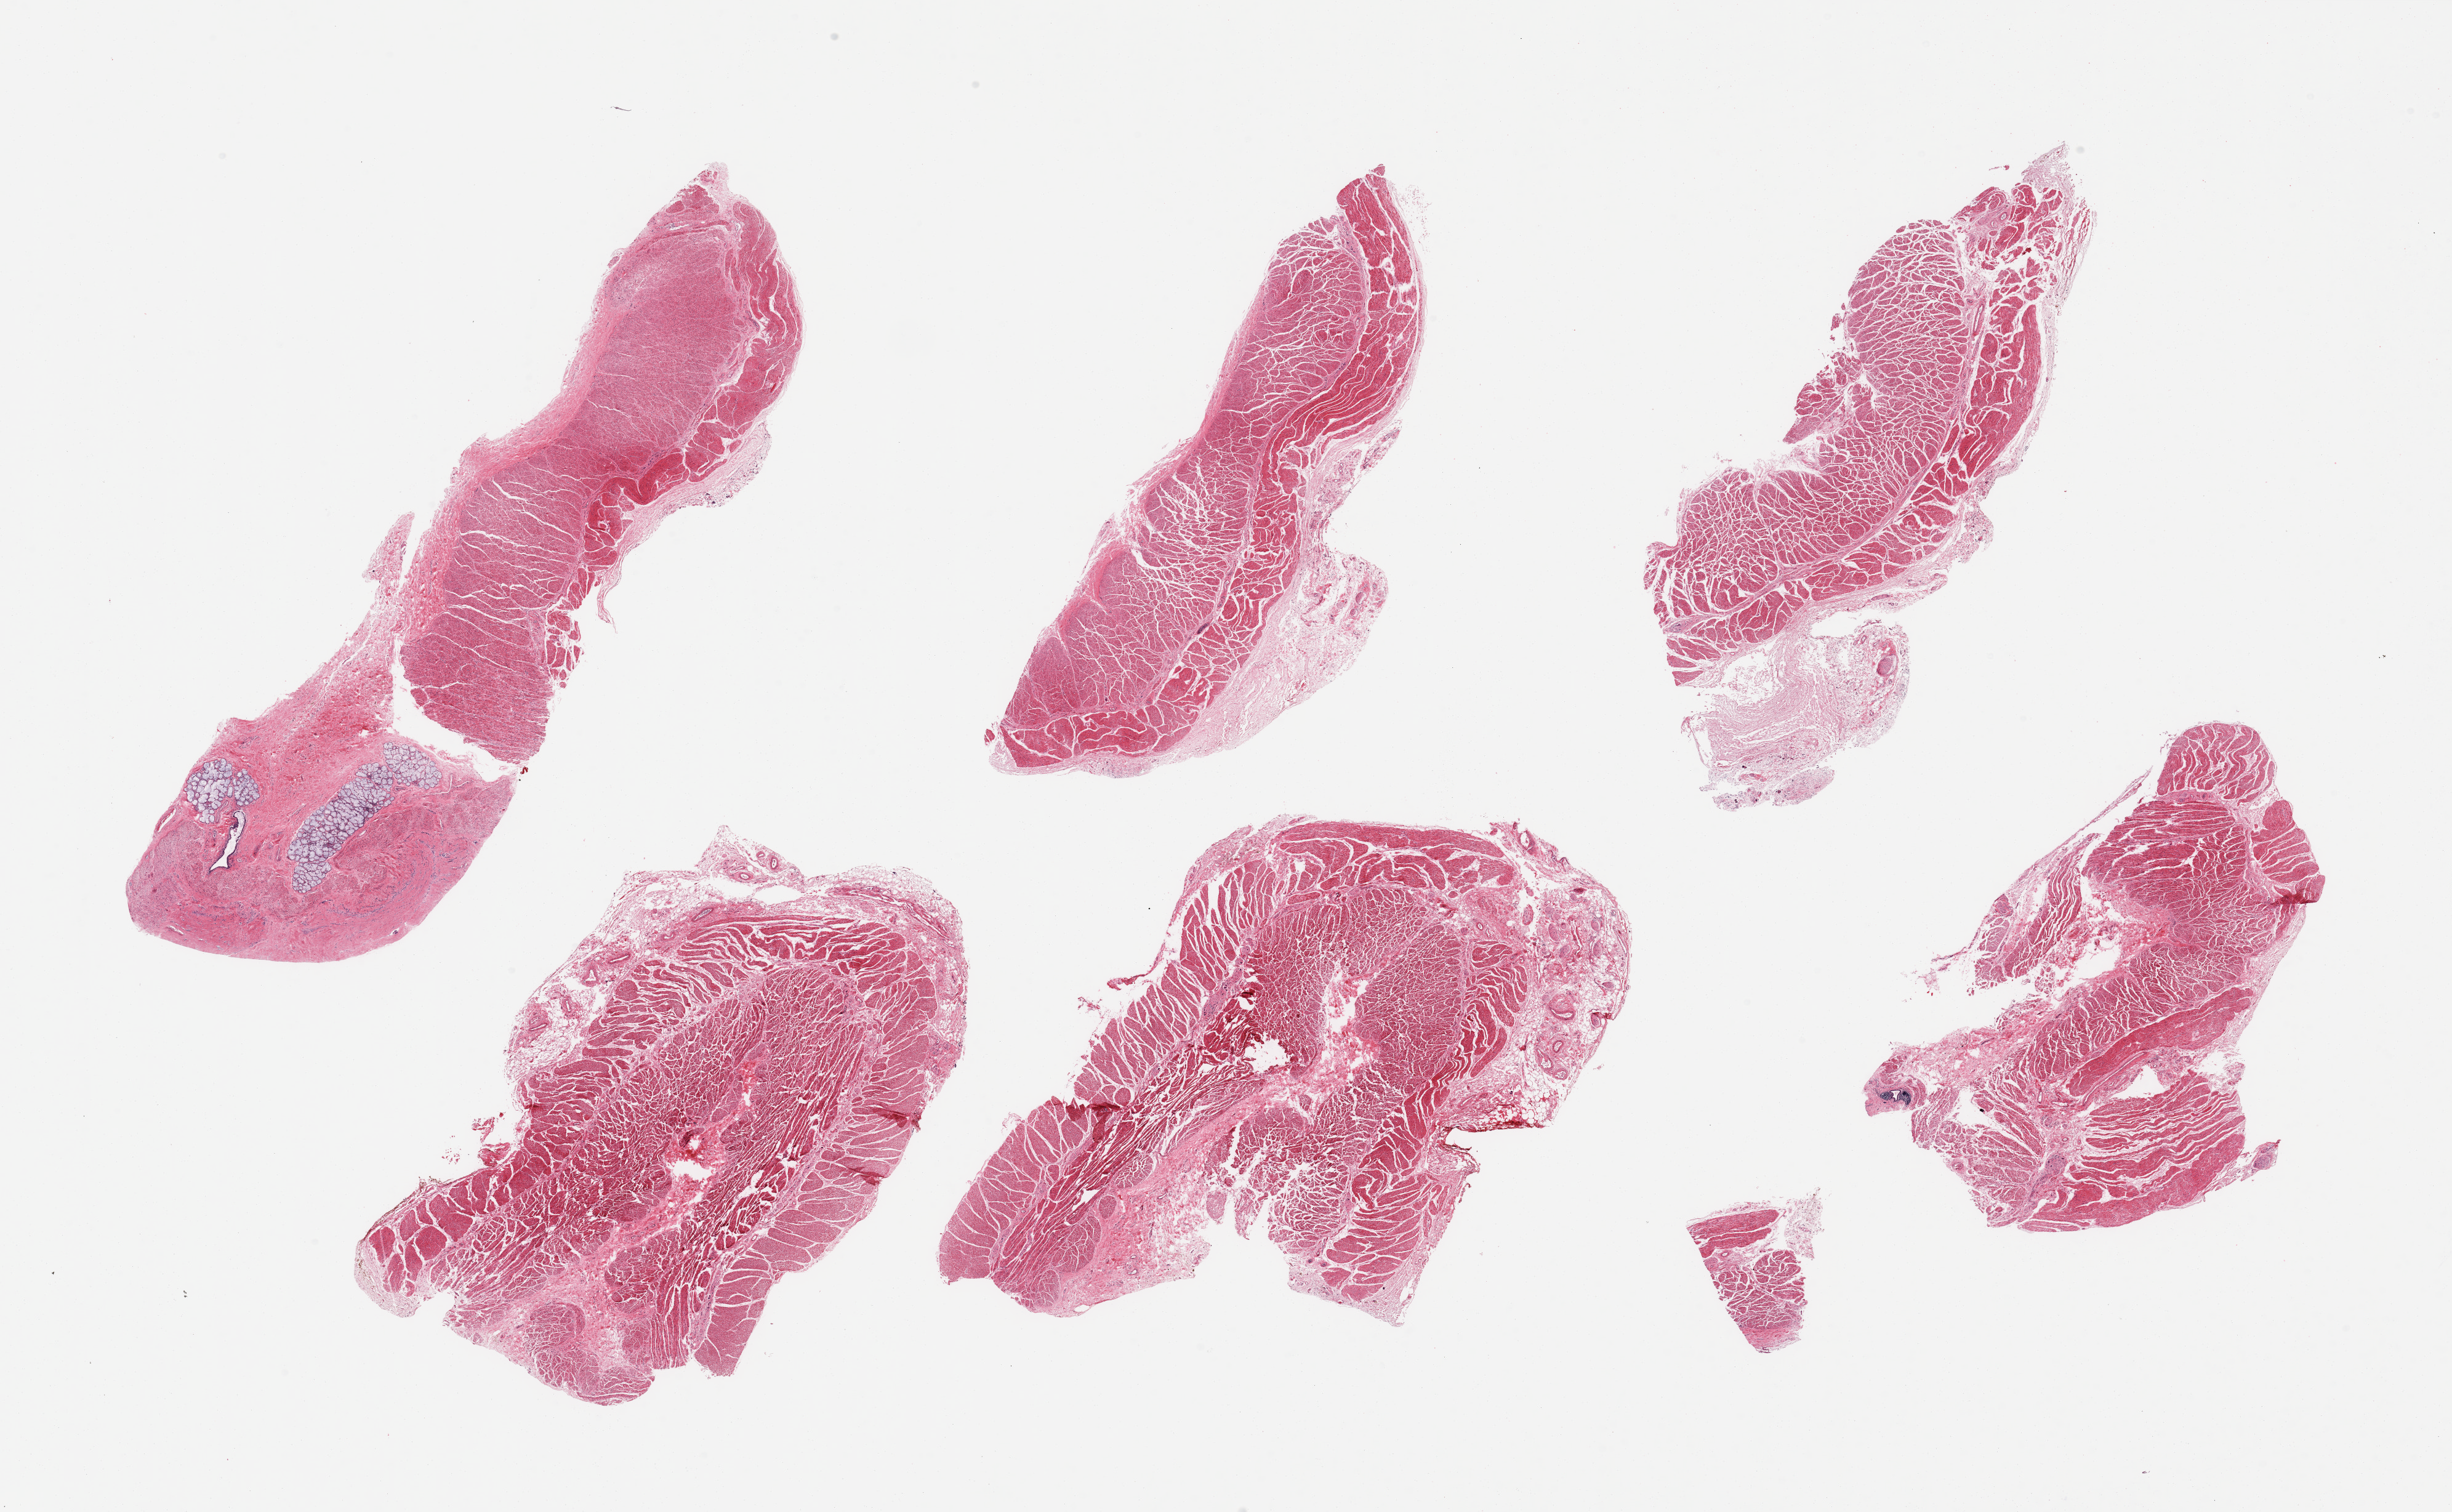
Whole-slide image, hematoxylin and eosin (H&E) stain — shown as a low-resolution overview of the whole scanned area (about 31.5 x 19.4 mm, slide scanned at 20x), PAXgene-fixed, paraffin-embedded tissue, sampled site (target tissue): esophageal muscle, donor tissue sample. Donor sex: female.
Pathologist's review note for this sample: 6 pieces; submucosal fibrovascular tissue in all, up to 3.5 mm across, 1 with submucosal glands.